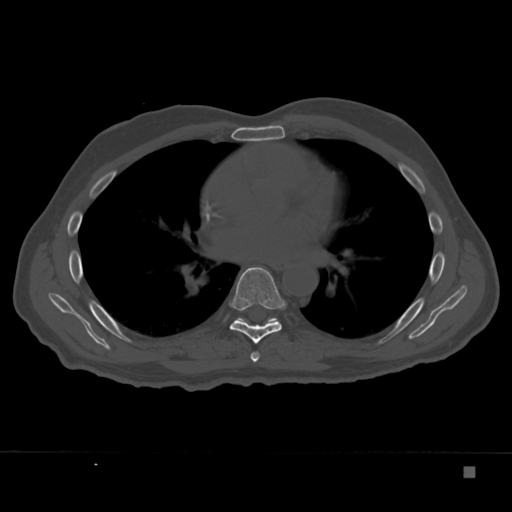
CT including the spine, one axial slice; position 222 of 332 along the scan axis; reconstruction kernel Br40s; bone window (W 1800 / L 400 HU); 512 × 512 image matrix, field of view 389 × 389 mm. Patient: male, 72 years. From the clinical record (not read from this slice): primary cancer: skeletal.
Outlined on this slice (semi-automatically segmented with operator editing):
- T6 vertebra: bounding box [x1, y1, x2, y2] px = [251, 352, 260, 362]
- T7 vertebra: [230, 267, 284, 344]
- T8 vertebra: [237, 318, 278, 322]